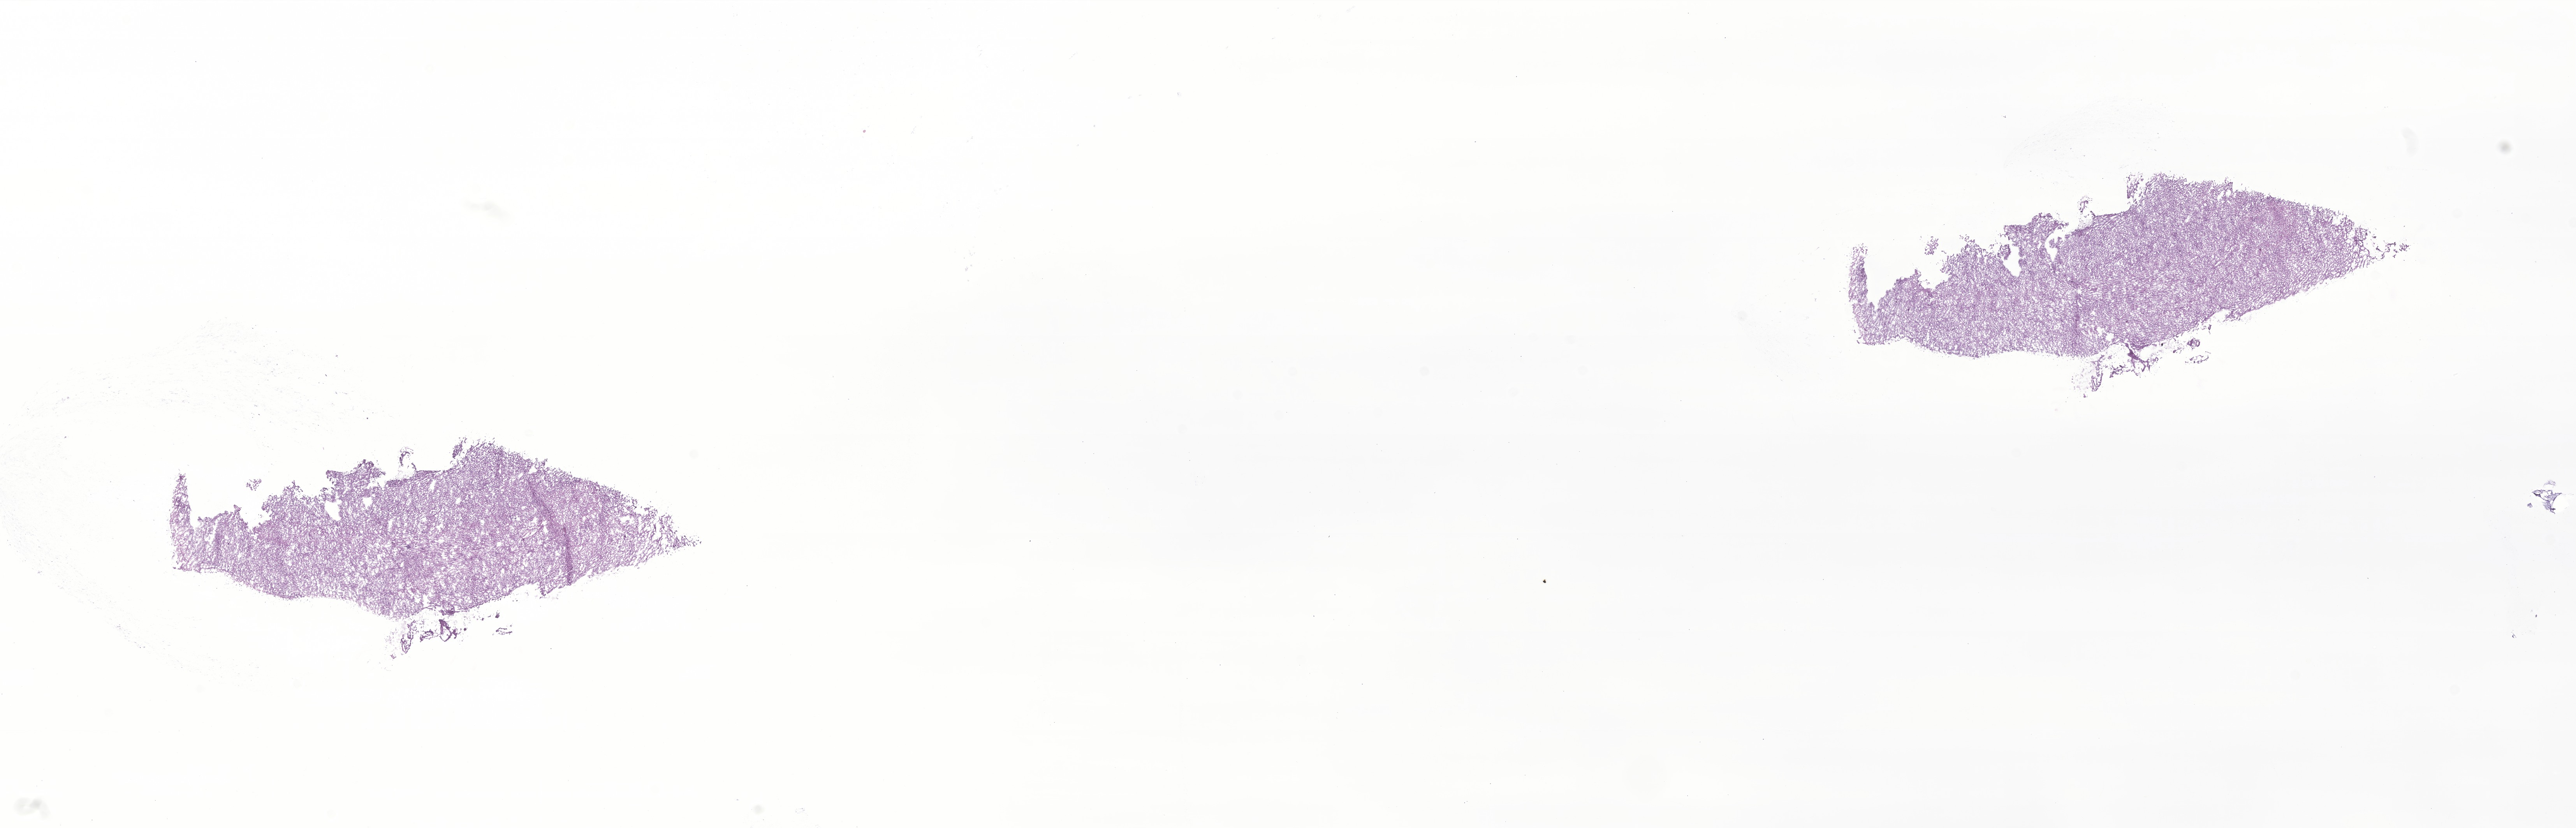
Digitized haematoxylin and eosin-stained section of tumor tissue from the cerebellum, shown as a low-resolution overview of the whole scanned area (about 27.9 x 9.0 mm), cryosection (OCT / tissue freezing medium). Patient: male, age 338 days.
- diagnosis (ICD-O-3 morphology term): Glioma, malignant